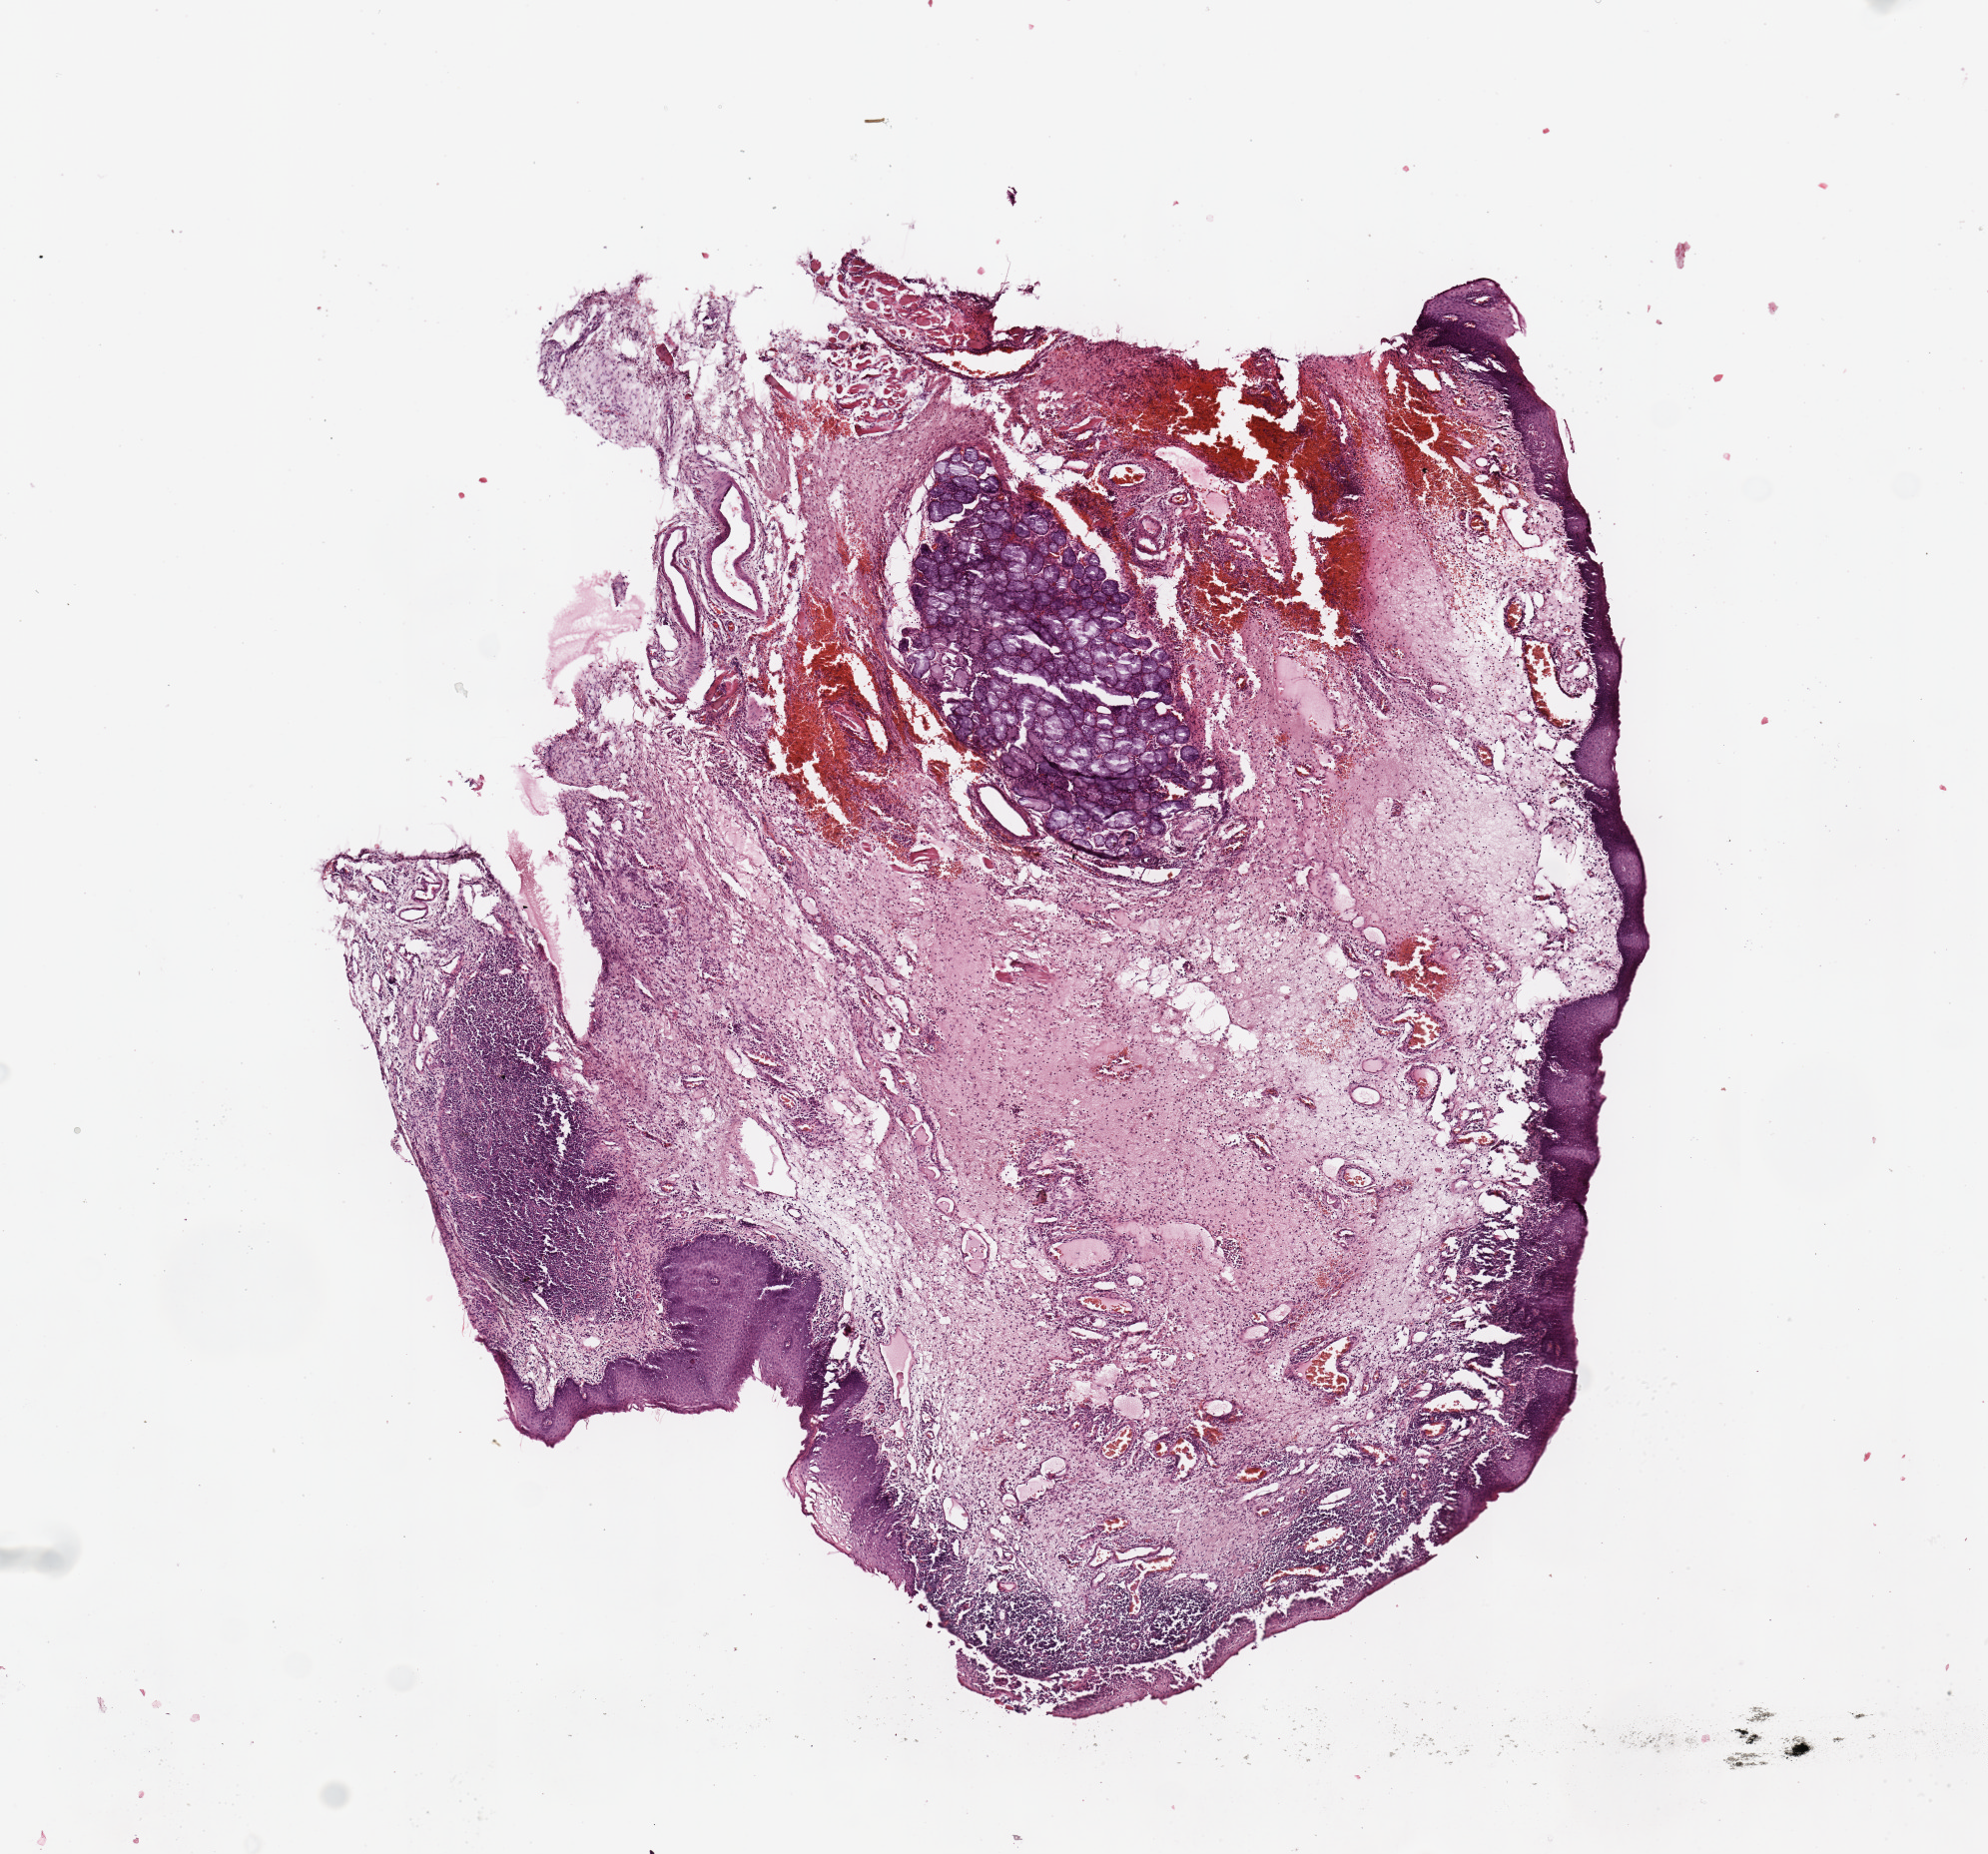
H&E-stained whole-slide image — a low-resolution overview of the entire scanned area, about 7.9 x 7.3 mm; normal (non-tumour) tissue sample, sampled site: oropharynx. Patient: male, age 51 years.
This section: normal (non-tumour) tissue from the same patient. Patient diagnosis: Squamous cell carcinoma, NOS (oropharynx, NOS).